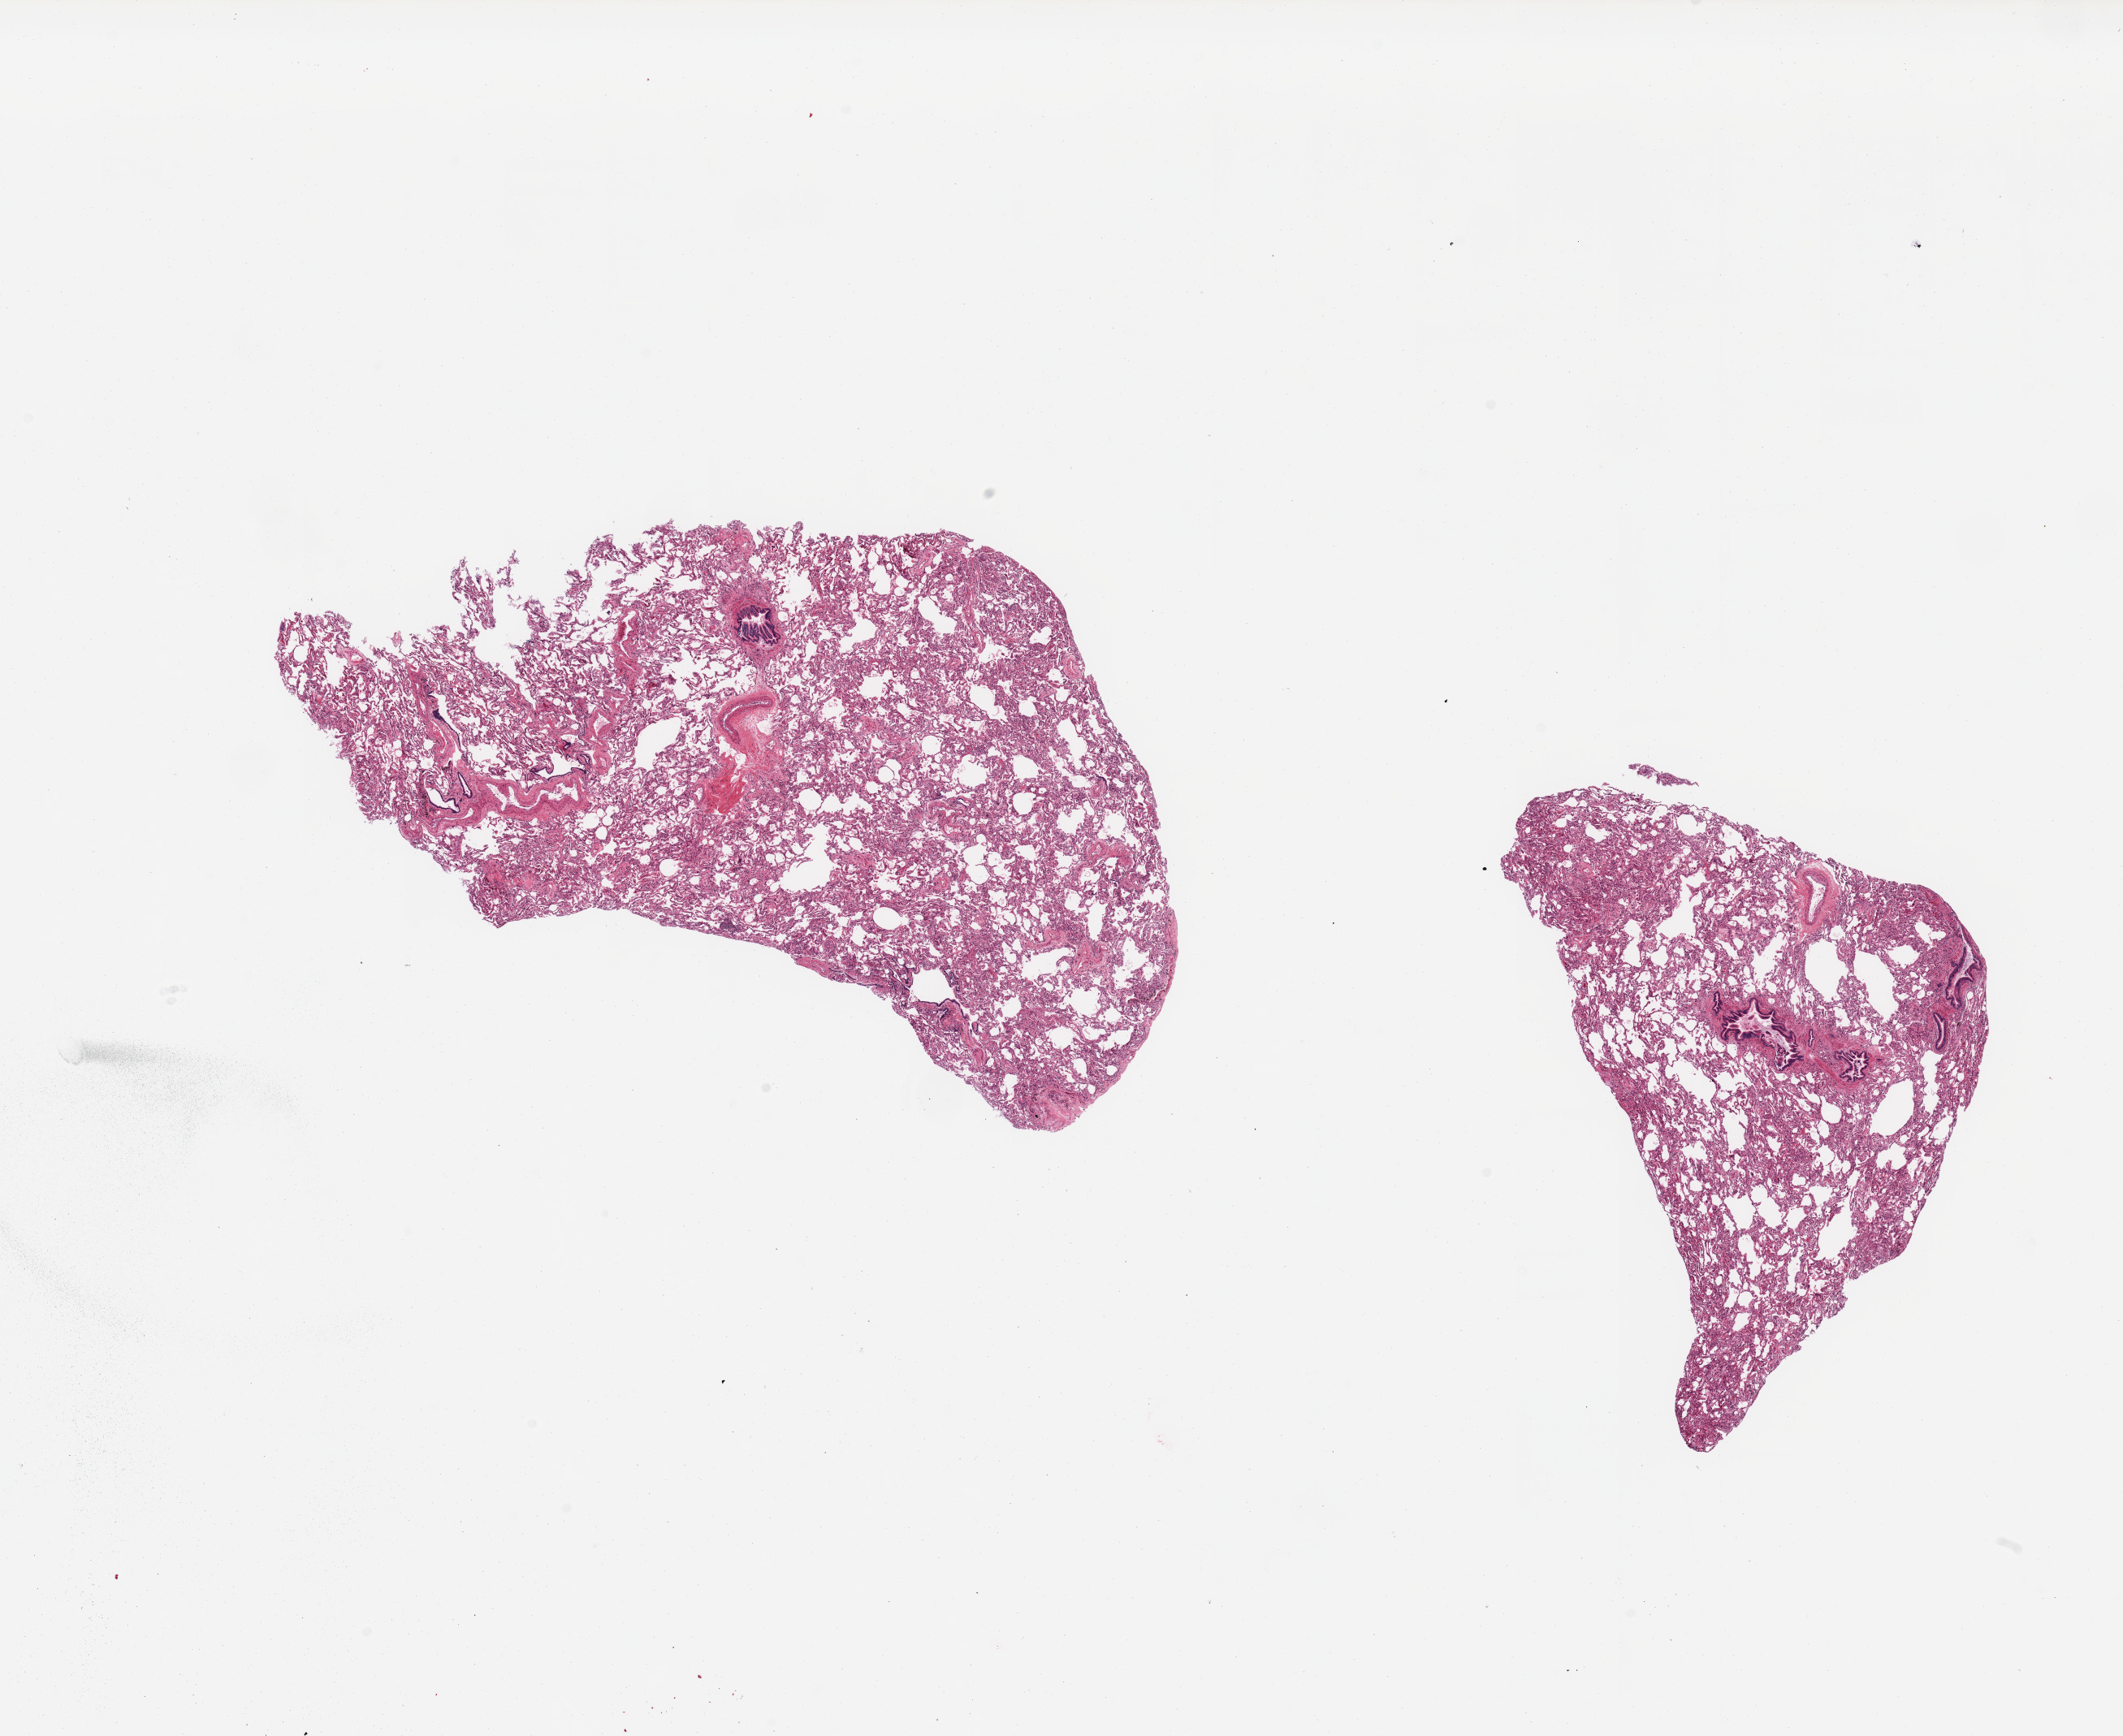
Haematoxylin and eosin whole-slide image, brightfield, shown as a low-resolution overview of the whole scanned area (about 20.7 x 16.9 mm); PAXgene-fixed paraffin-embedded (PFPE) section; sampled site (target tissue): lung; donor tissue sample. Donor: female.
Reviewer comment on this tissue sample: 2 pieces; congestion and focal alveolar collapse; thick walled vessels.